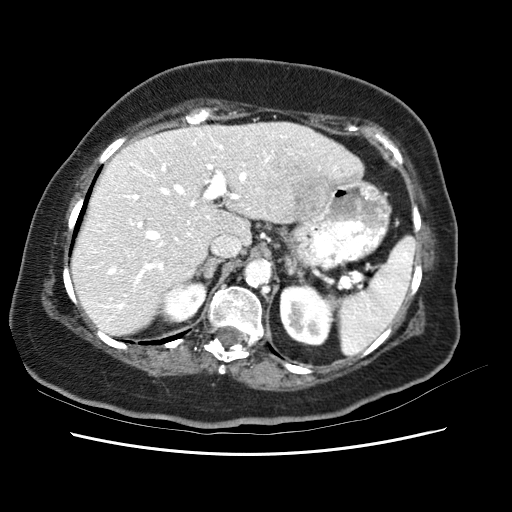
Contrast-enhanced abdominal CT (liver protocol), one axial slice. Position 42 of 62 along the scan axis. Reconstruction kernel STANDARD. 120 kVp. Soft-tissue window (W 400 / L 40 HU). 2.5 mm slice thickness. 512 × 512 image matrix, field of view 340 × 340 mm. From the clinical record (not read from this slice): diagnosis: hepatocellular carcinoma (patient treated with transarterial chemoembolisation; whether this scan precedes or follows treatment is not stated here); TNM stage (as recorded): Stage-I; Child-Pugh class: B; tumour nodularity: uninodular; tumour size: 5.3 cm.
Structures marked on this image (semi-automatic segmentation, software-assisted and operator-edited):
- liver parenchyma outside the tumour (the mass and vessels are separate outlines, so this box may not span the whole liver): bounding box (x1, y1, x2, y2) in pixels: (74, 121, 360, 332)
- mass: (256, 144, 328, 224)
- liver vessels: (102, 131, 336, 321)